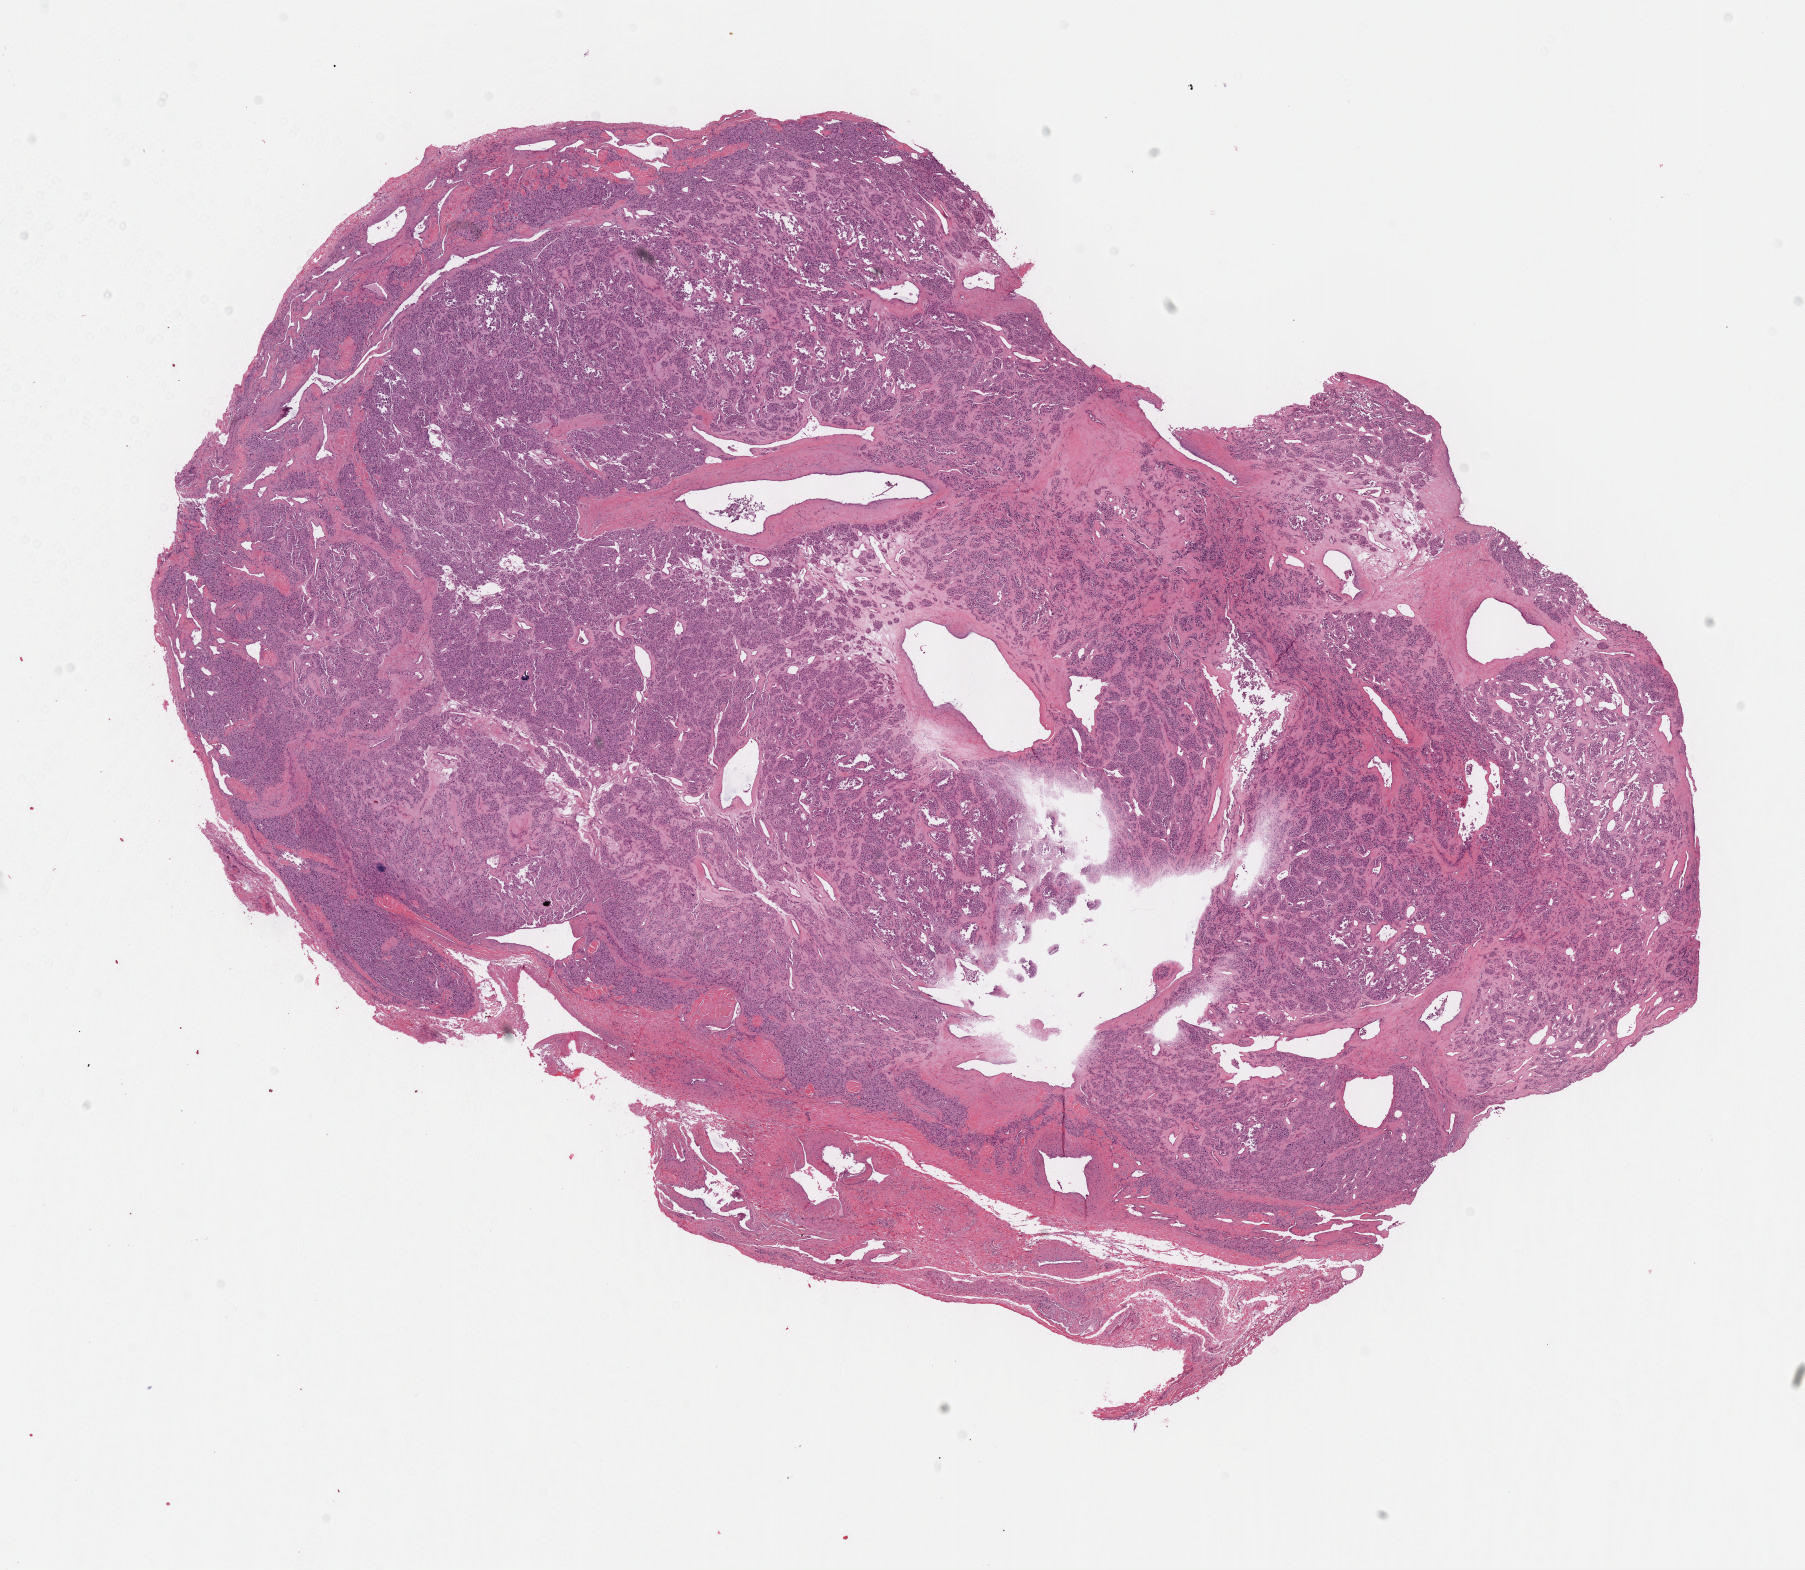
Hematoxylin and eosin (H&E) stained whole-slide image, low-resolution overview of the scanned area, about 14.6 x 12.7 mm (acquisition: 40x scan); formalin-fixed paraffin-embedded (FFPE) diagnostic section; primary tumour sample. Patient: female, age at initial diagnosis 41 years.
Diagnosis: Extra-adrenal paraganglioma, malignant.